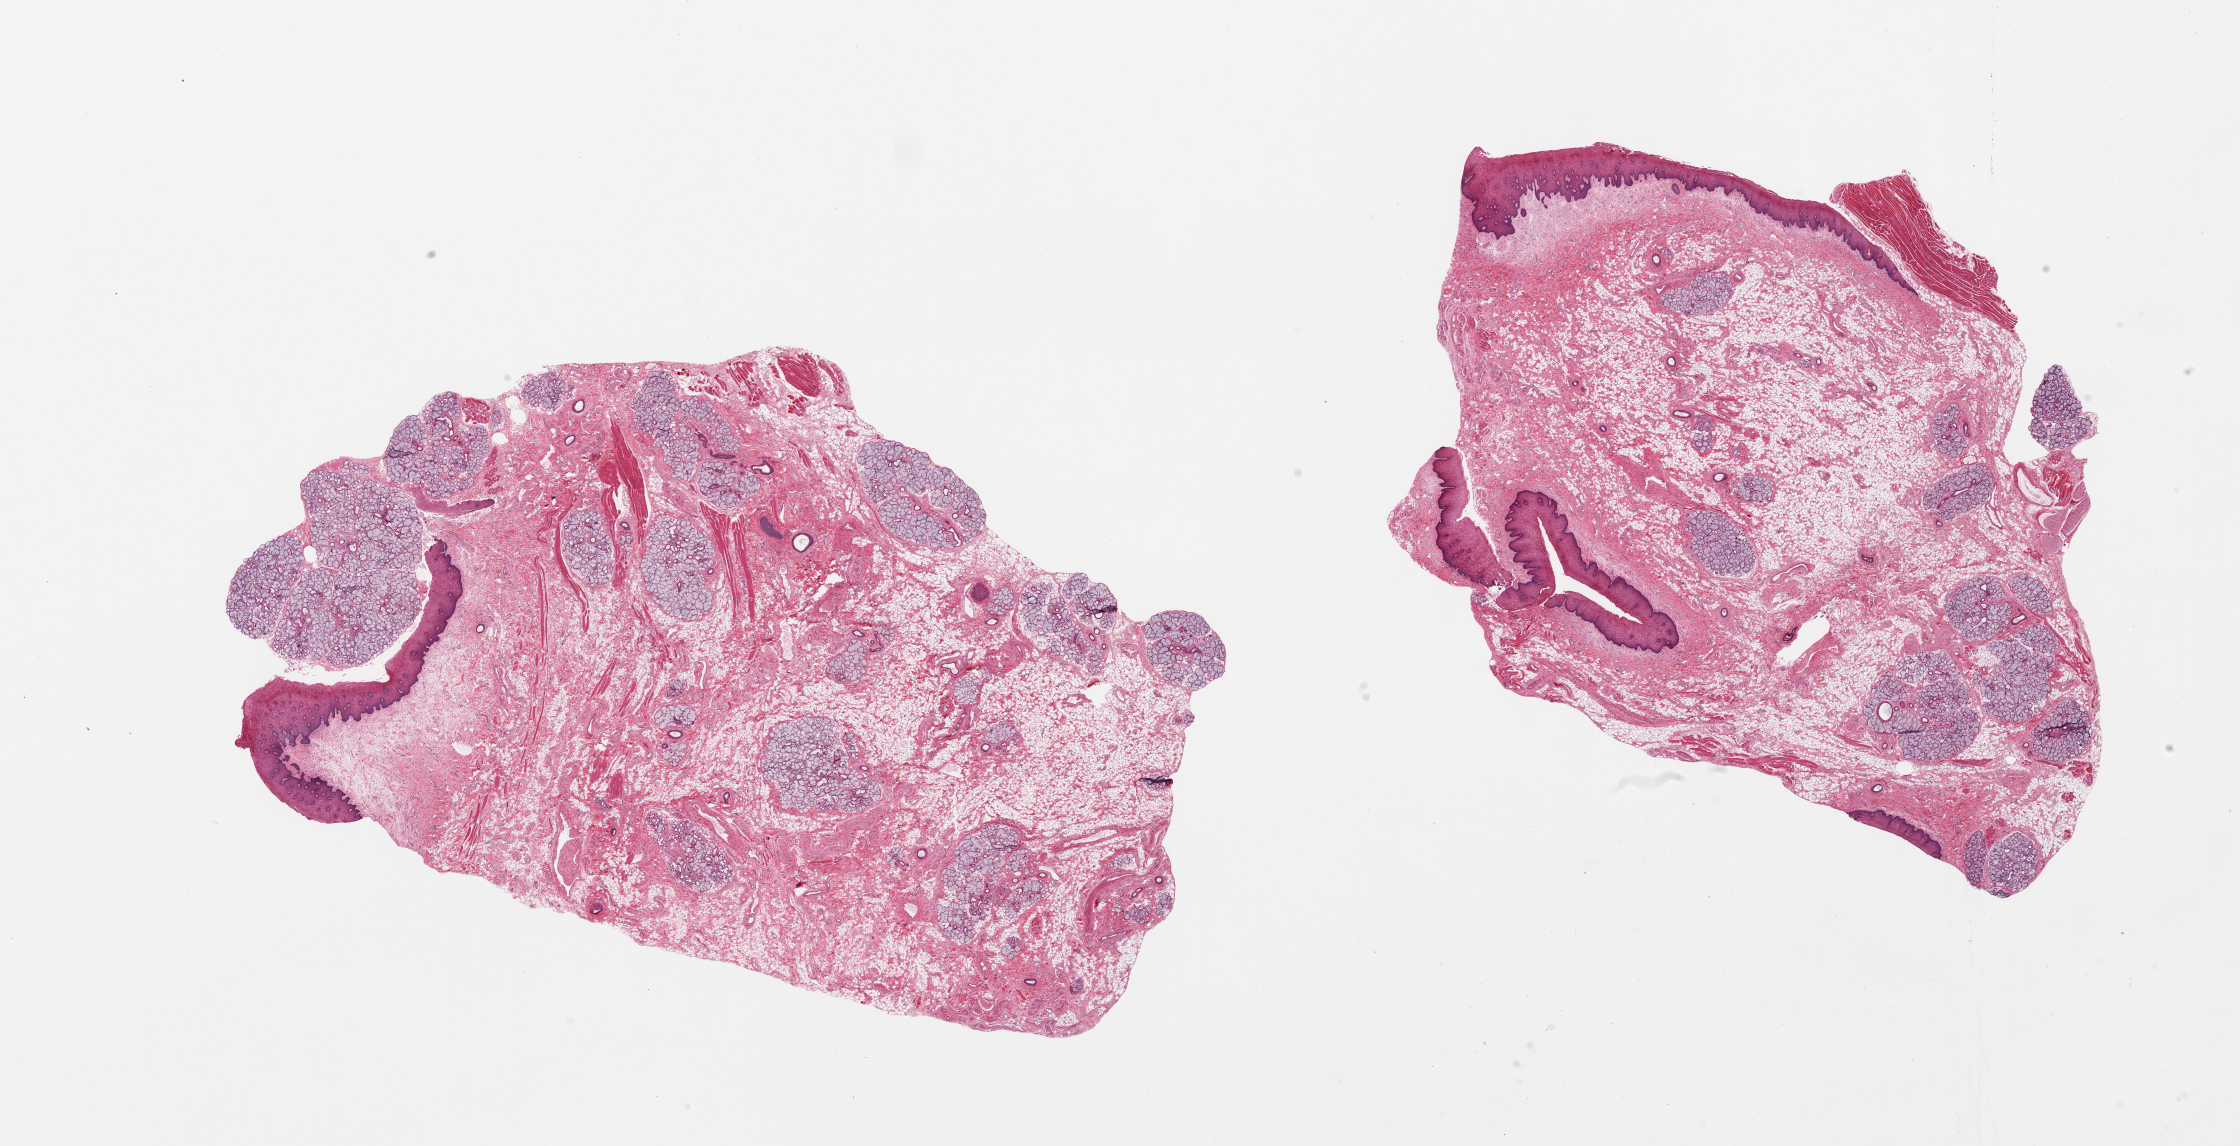
Digitized haematoxylin and eosin-stained section, brightfield — a low-resolution overview of the entire scanned area, about 35.4 x 18.1 mm (slide scanned at 20x). PAXgene-fixed paraffin-embedded (PFPE) section. Target tissue: minor salivary gland. Donor tissue sample.
Pathologist's review note for this sample: 2 pieces, slivary gland represents 20-30% of the tissue, rest is squamous mucosa, stroma, fat and skeletal muscle; focal minimal acute and chronic inflammation.